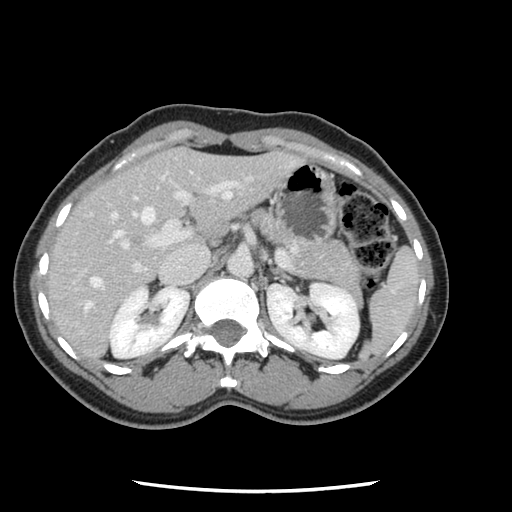
Contrast-enhanced abdominal CT, one axial slice. Position 74 of 134 along the scan axis. Soft-tissue window (W 400 / L 40 HU). 2.5 mm slice thickness. 512 × 512 image matrix, field of view 330 × 330 mm. Female patient, age 43 years. Case-level facts recorded for this patient, not image findings: diagnosis: colorectal cancer liver metastases, imaged before liver resection; multiple liver metastases: yes; largest metastasis: 3.4 cm; disease in both lobes: yes.
Structures marked on this image (manually delineated by an expert):
- hepatic veins: box from (x=85, y=192) to (x=231, y=311) px
- liver: (x=47, y=148)–(x=296, y=359)
- planned liver remnant (the part of the liver to remain after resection): (x=47, y=150)–(x=187, y=304)
- portal vein (with intrahepatic branches): (x=73, y=181)–(x=239, y=284)